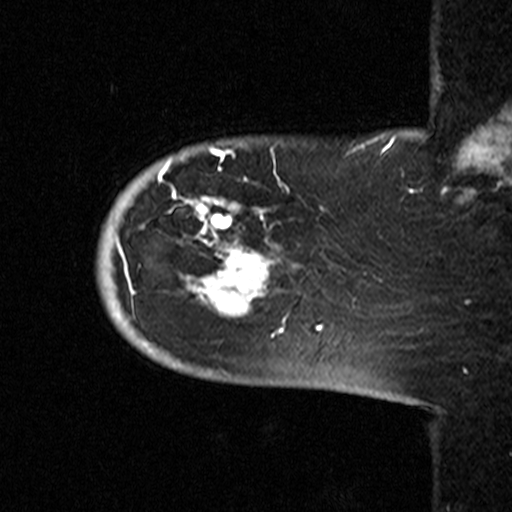
Breast MRI (dynamic contrast-enhanced), one sagittal slice; position 7 of 44 along the scan axis; dynamic contrast-enhanced study with each time point stored as its own series, time point 2 of 3 at this slice position (early post-contrast, ordered by acquisition time); 1.5 T; TE 4.5 ms, TR 11 ms; 3.27 mm slice thickness; 512 × 512 image matrix, field of view 200 × 200 mm. Female patient, age 53 years. Case-level facts recorded for this patient, not image findings: setting: breast cancer imaged before/during neoadjuvant chemotherapy; receptor status: HR-positive, HER2-negative.
Annotated regions visible in this slice (semi-automatically segmented with operator editing):
- analysis volume of interest (the breast-tissue region the enhancement analysis was run in; not a lesion): bounding box <89,154,311,367> (left, top, right, bottom; pixels)
- tumour enhancement mask (voxels above the 90 % enhancement threshold inside the analysis volume of interest): <116,154,290,338>